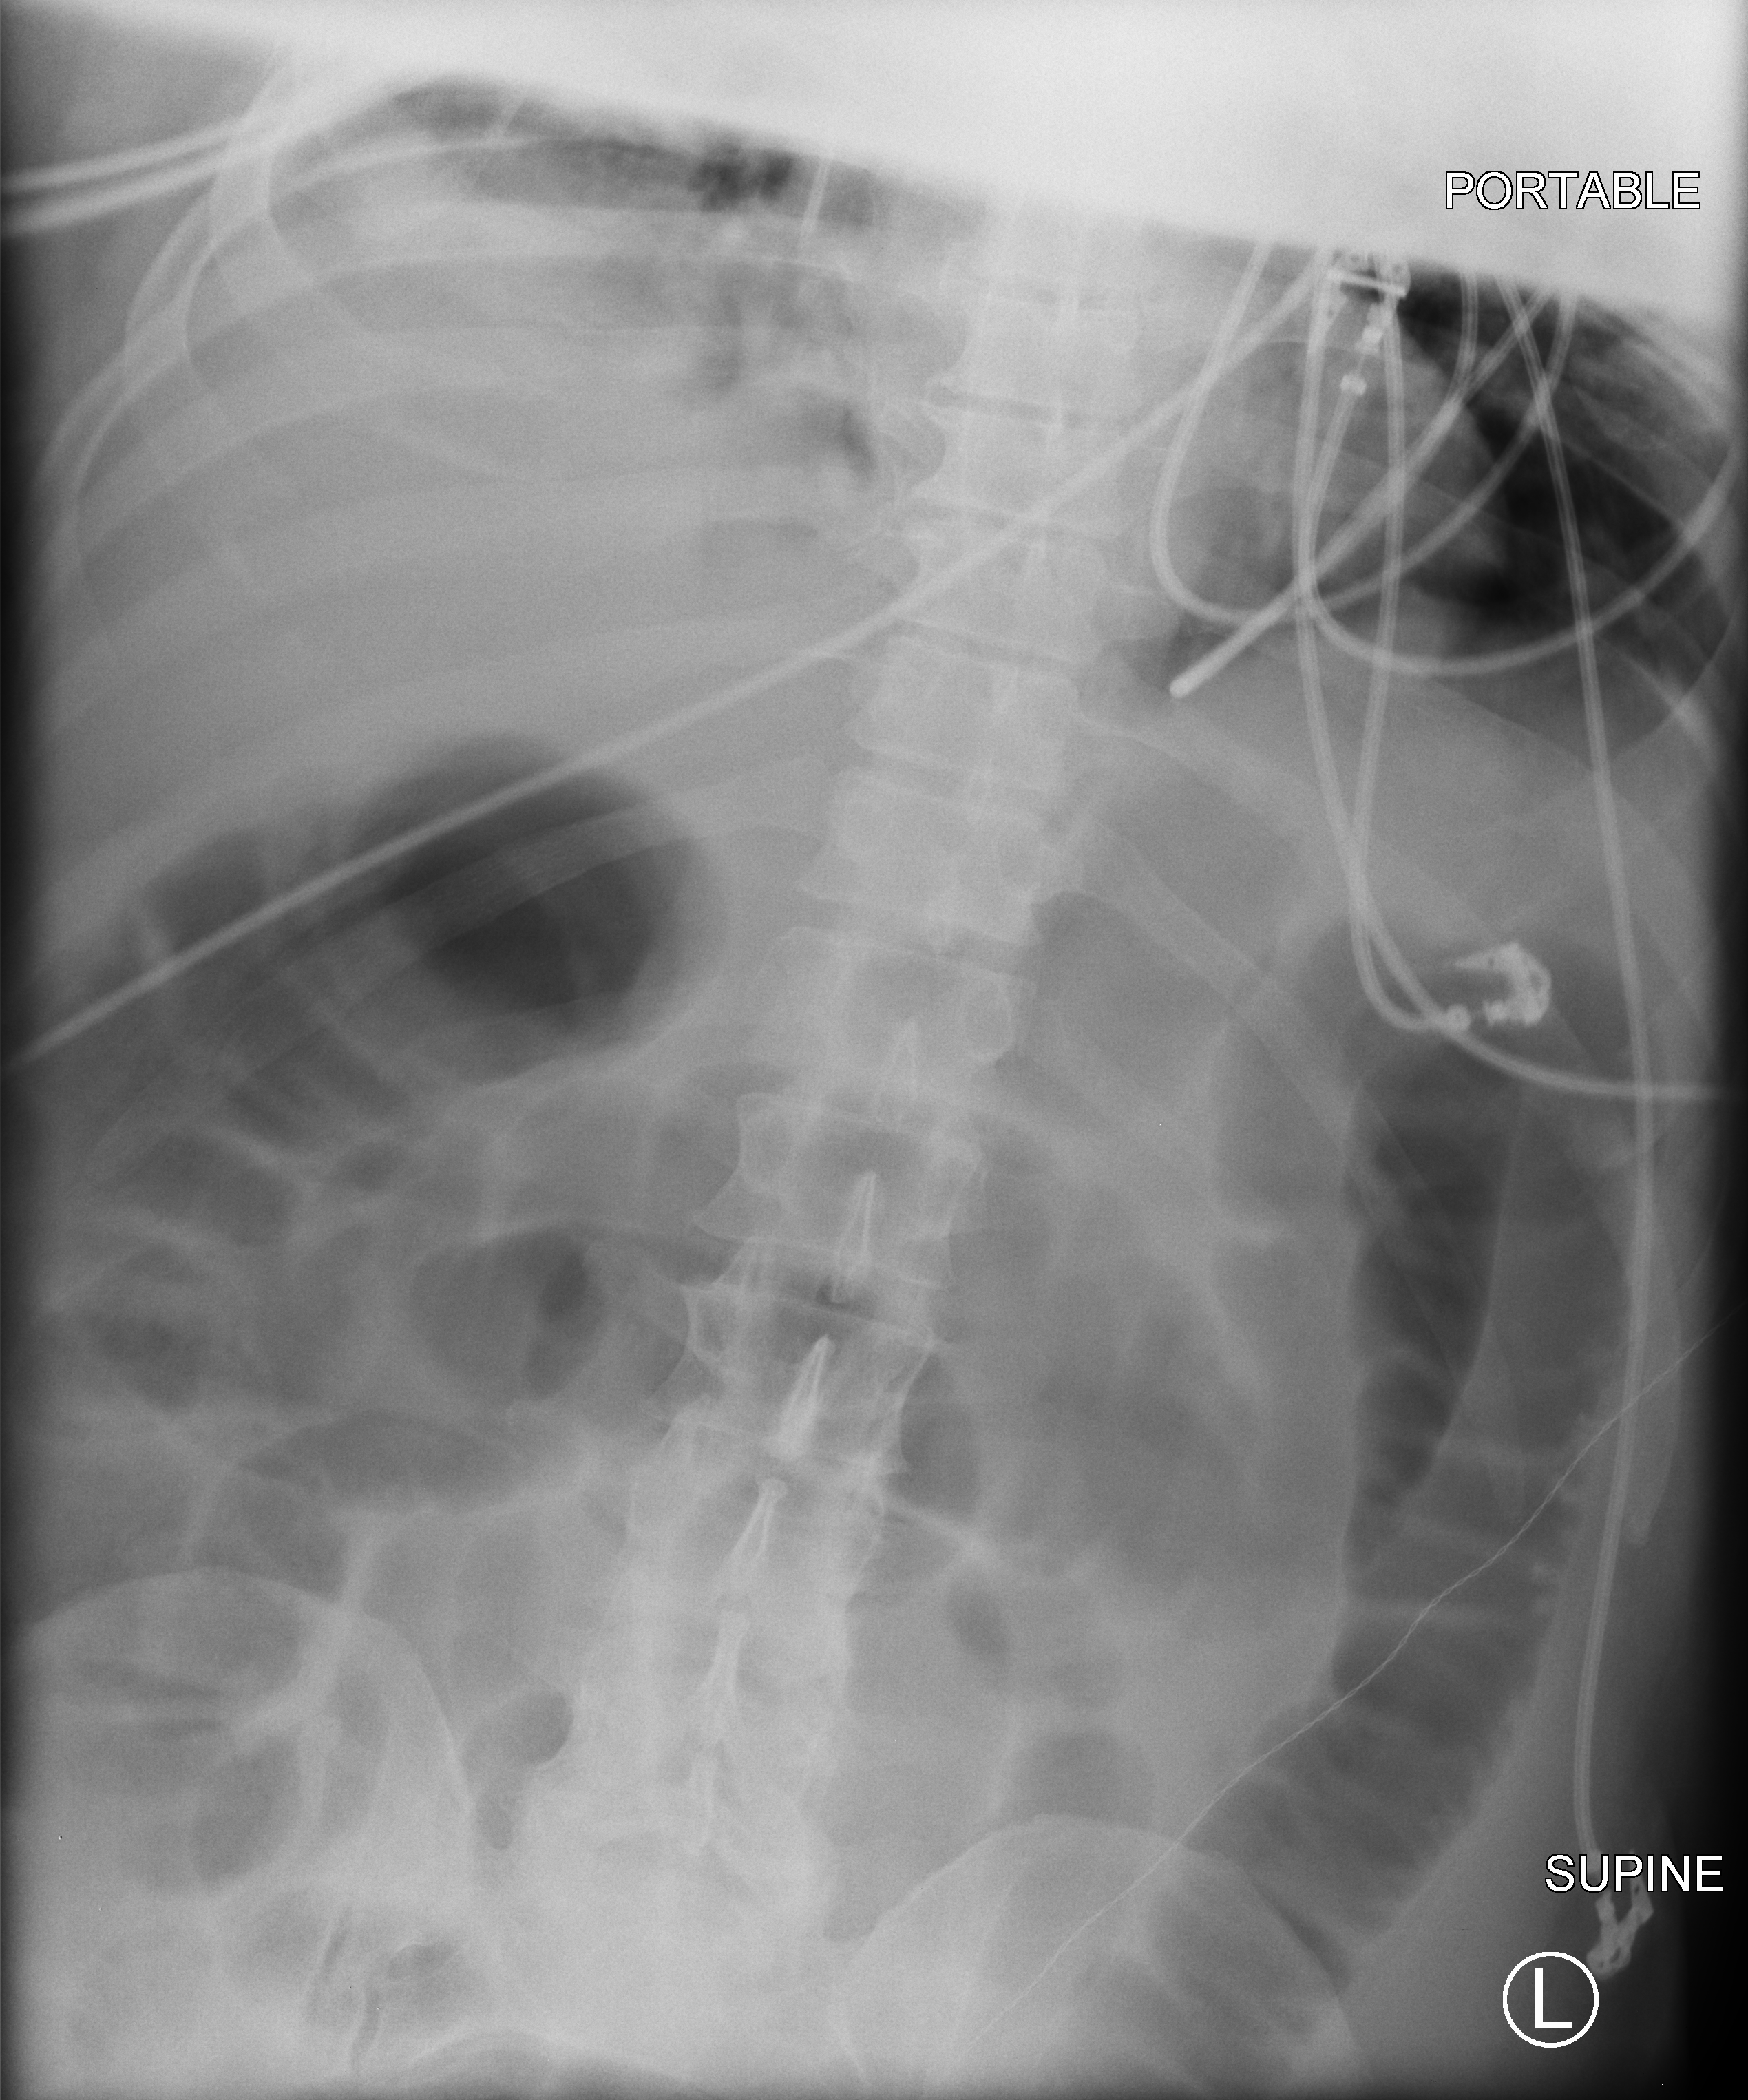
Portable abdomen radiograph, anteroposterior (AP) projection. Patient hospitalised with COVID-19; male, aged 18–59 years.
Hospital-stay facts (about this admission, not read from this image; timing relative to this image not recorded):
- mechanically ventilated during this hospital stay: yes